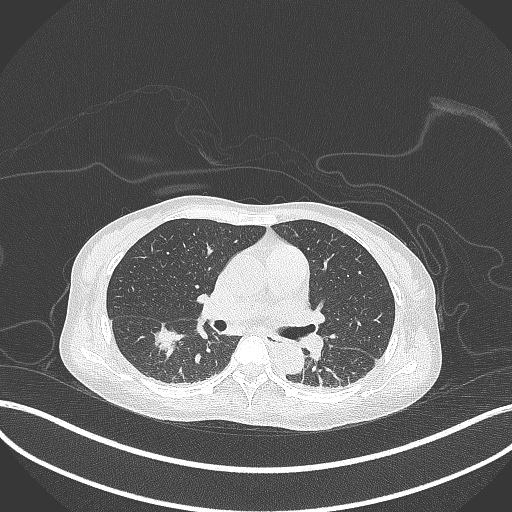
Chest CT, one axial slice; position 172 of 261 along the scan axis; reconstruction kernel B70f; 120 kVp; lung window (W 1500 / L -600 HU); 1 mm slice thickness; 512 × 512 image matrix. Patient: female, 44 years. From the clinical record (not read from this slice): clinical TNM (as recorded): T1c N0 M0.
Outlined on this slice (rectangle marked by the reading radiologist):
- lung tumour (recorded histology: adenocarcinoma): bounding box (x1, y1, x2, y2) in pixels: (148, 324, 187, 357)